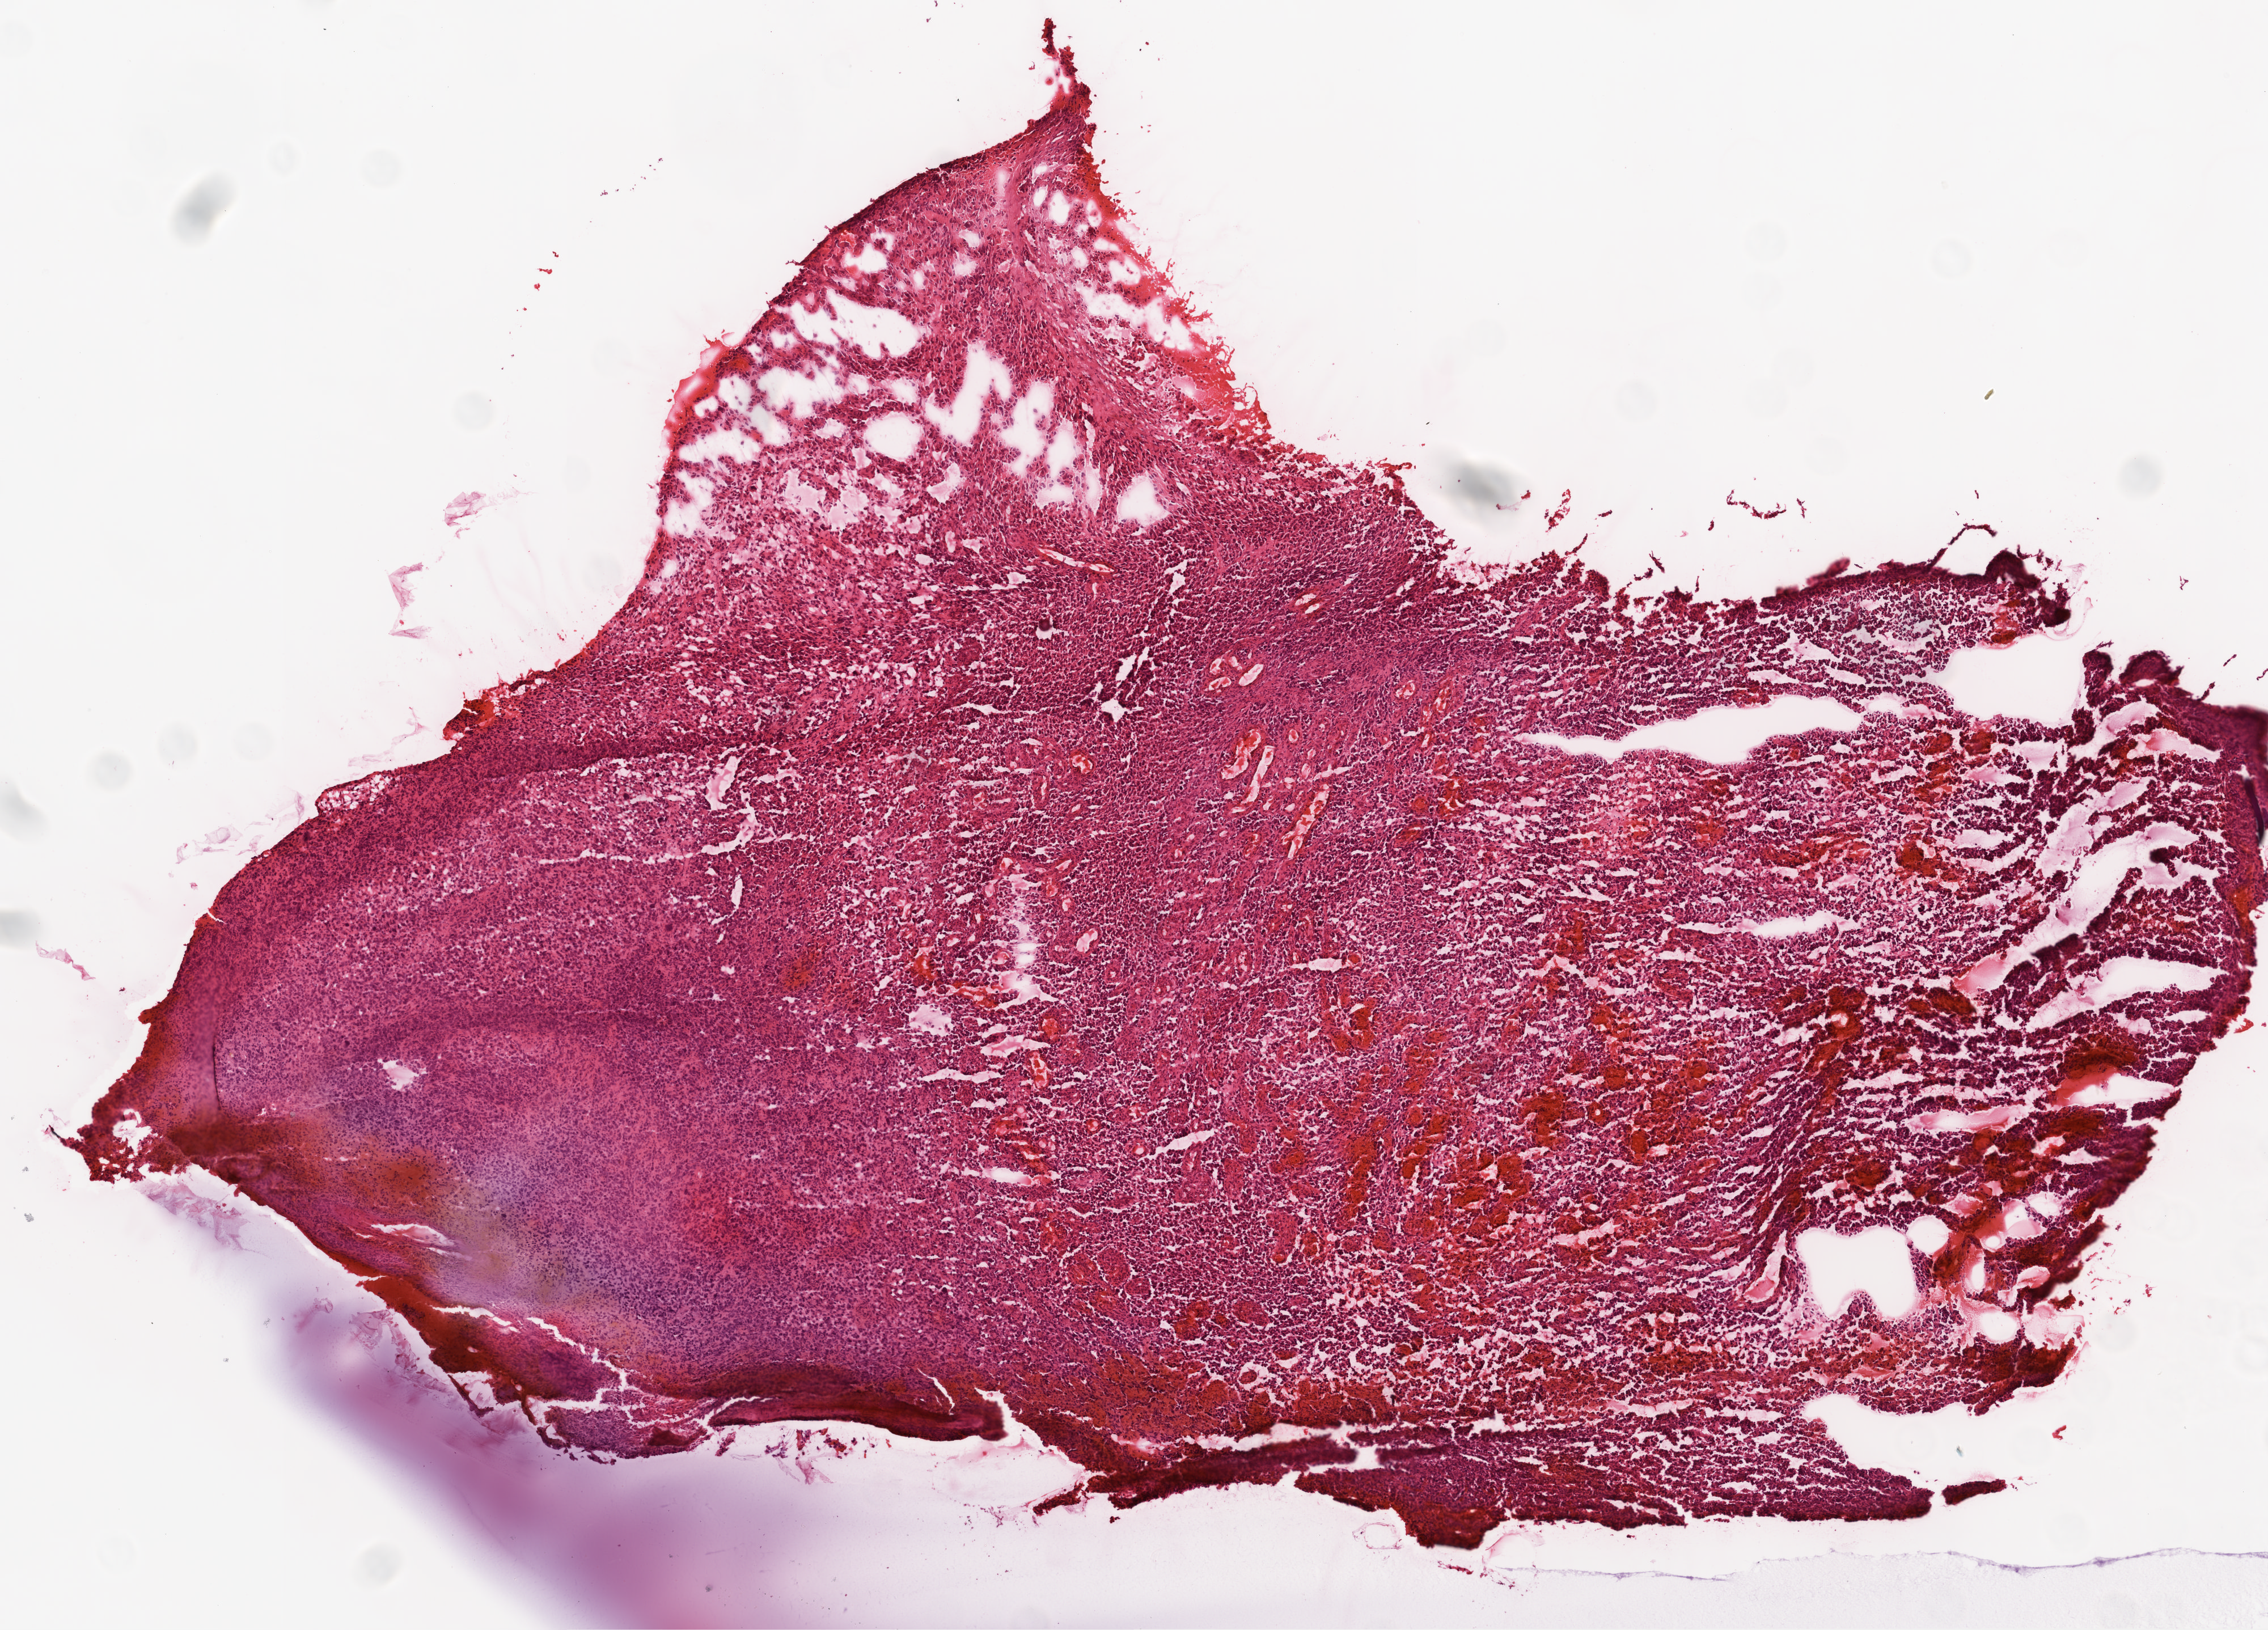
Digitized H&E tissue section (whole slide) — low-resolution overview of the scanned area, about 8.0 x 5.8 mm, frozen section, primary tumour sample from the brain. Male patient; age at initial diagnosis 86 years. Pathologist review of this section (percent, as recorded): tumour cells 80%, tumour nuclei 80%, normal cells 0%, stromal cells 20%, necrosis 0%.
Pathologic diagnosis: Glioblastoma.